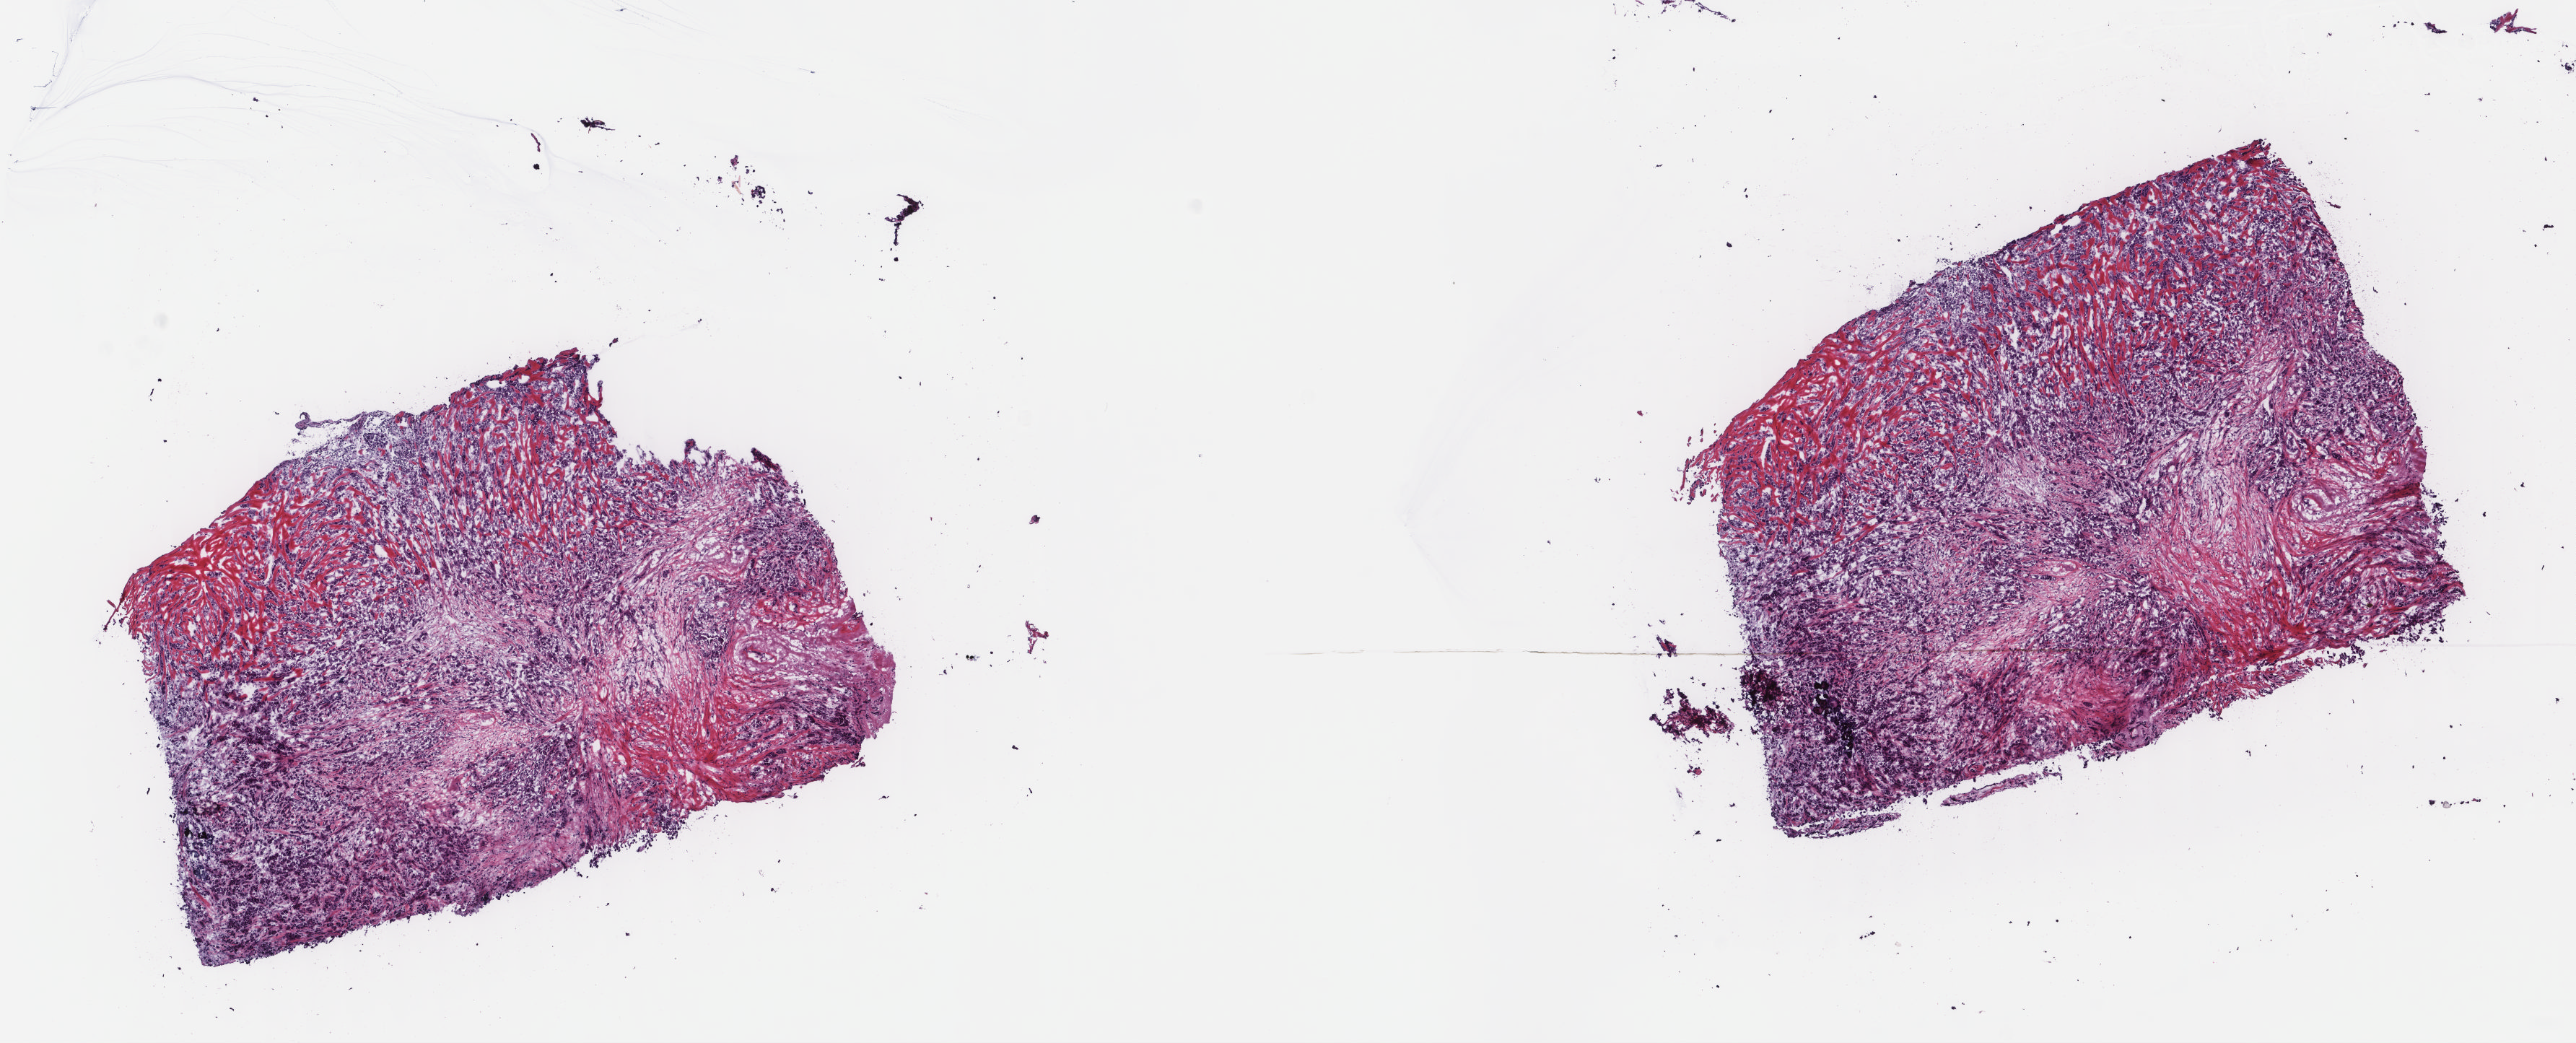
Digitized H&E tissue section (whole slide), shown as a low-resolution overview of the whole scanned area (about 14.2 x 5.7 mm), frozen section from the top of the tissue portion, breast, primary tumour sample. Female patient; age at initial diagnosis 48 years. Slide review estimates, as recorded: tumour cells 100%, tumour nuclei 92%, normal cells 0%, stromal cells 0%, necrosis 0%. Inflammatory infiltration, as recorded: lymphocyte infiltration 0%, monocyte infiltration 0%, neutrophil infiltration 0%.
Lymph nodes positive (case pathology): 0 of 6 examined. AJCC pathologic stage: IA (7th edition). Diagnosis: Infiltrating duct carcinoma, NOS. TNM: T1c N0 M0.